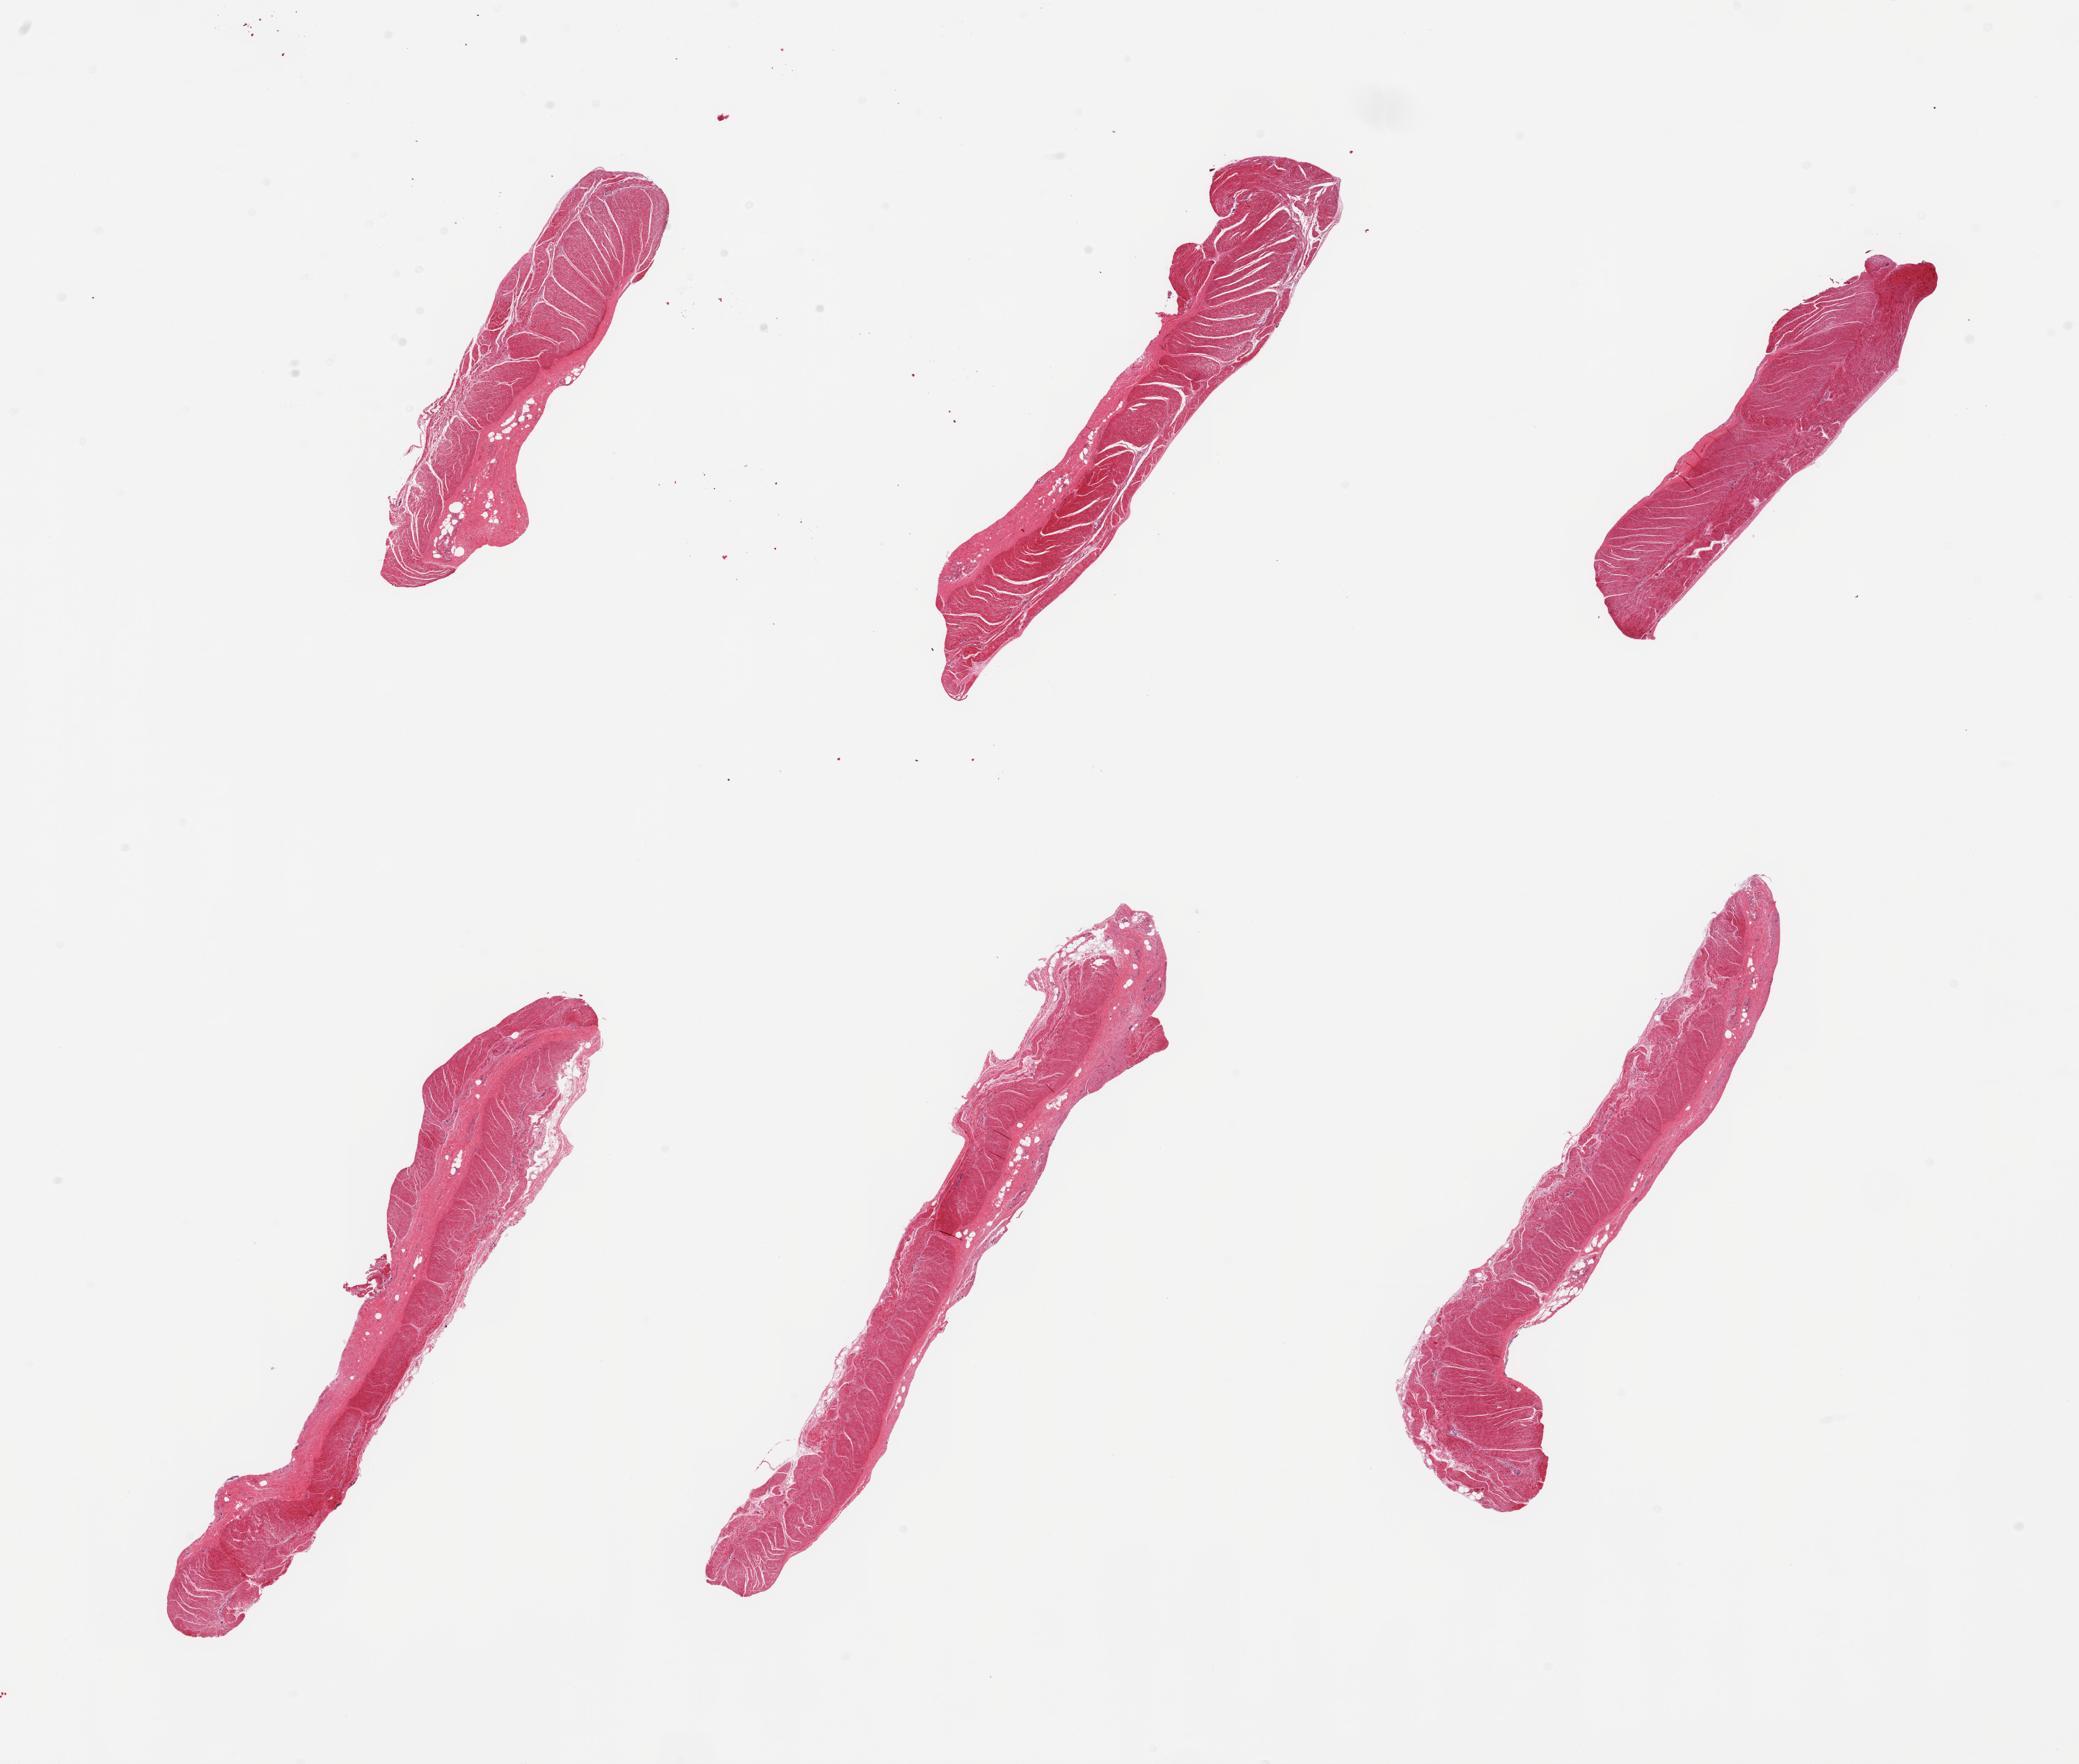
Whole-slide image, haematoxylin and eosin stain — low-resolution overview of the scanned area, about 23.6 x 20.0 mm (from a 20x scan). PAXgene-fixed, paraffin-embedded tissue. Section of sigmoid colon (target tissue). Tissue donor sample. Female donor.
Review note (as recorded): 6 pieces, confirmed target tissue.